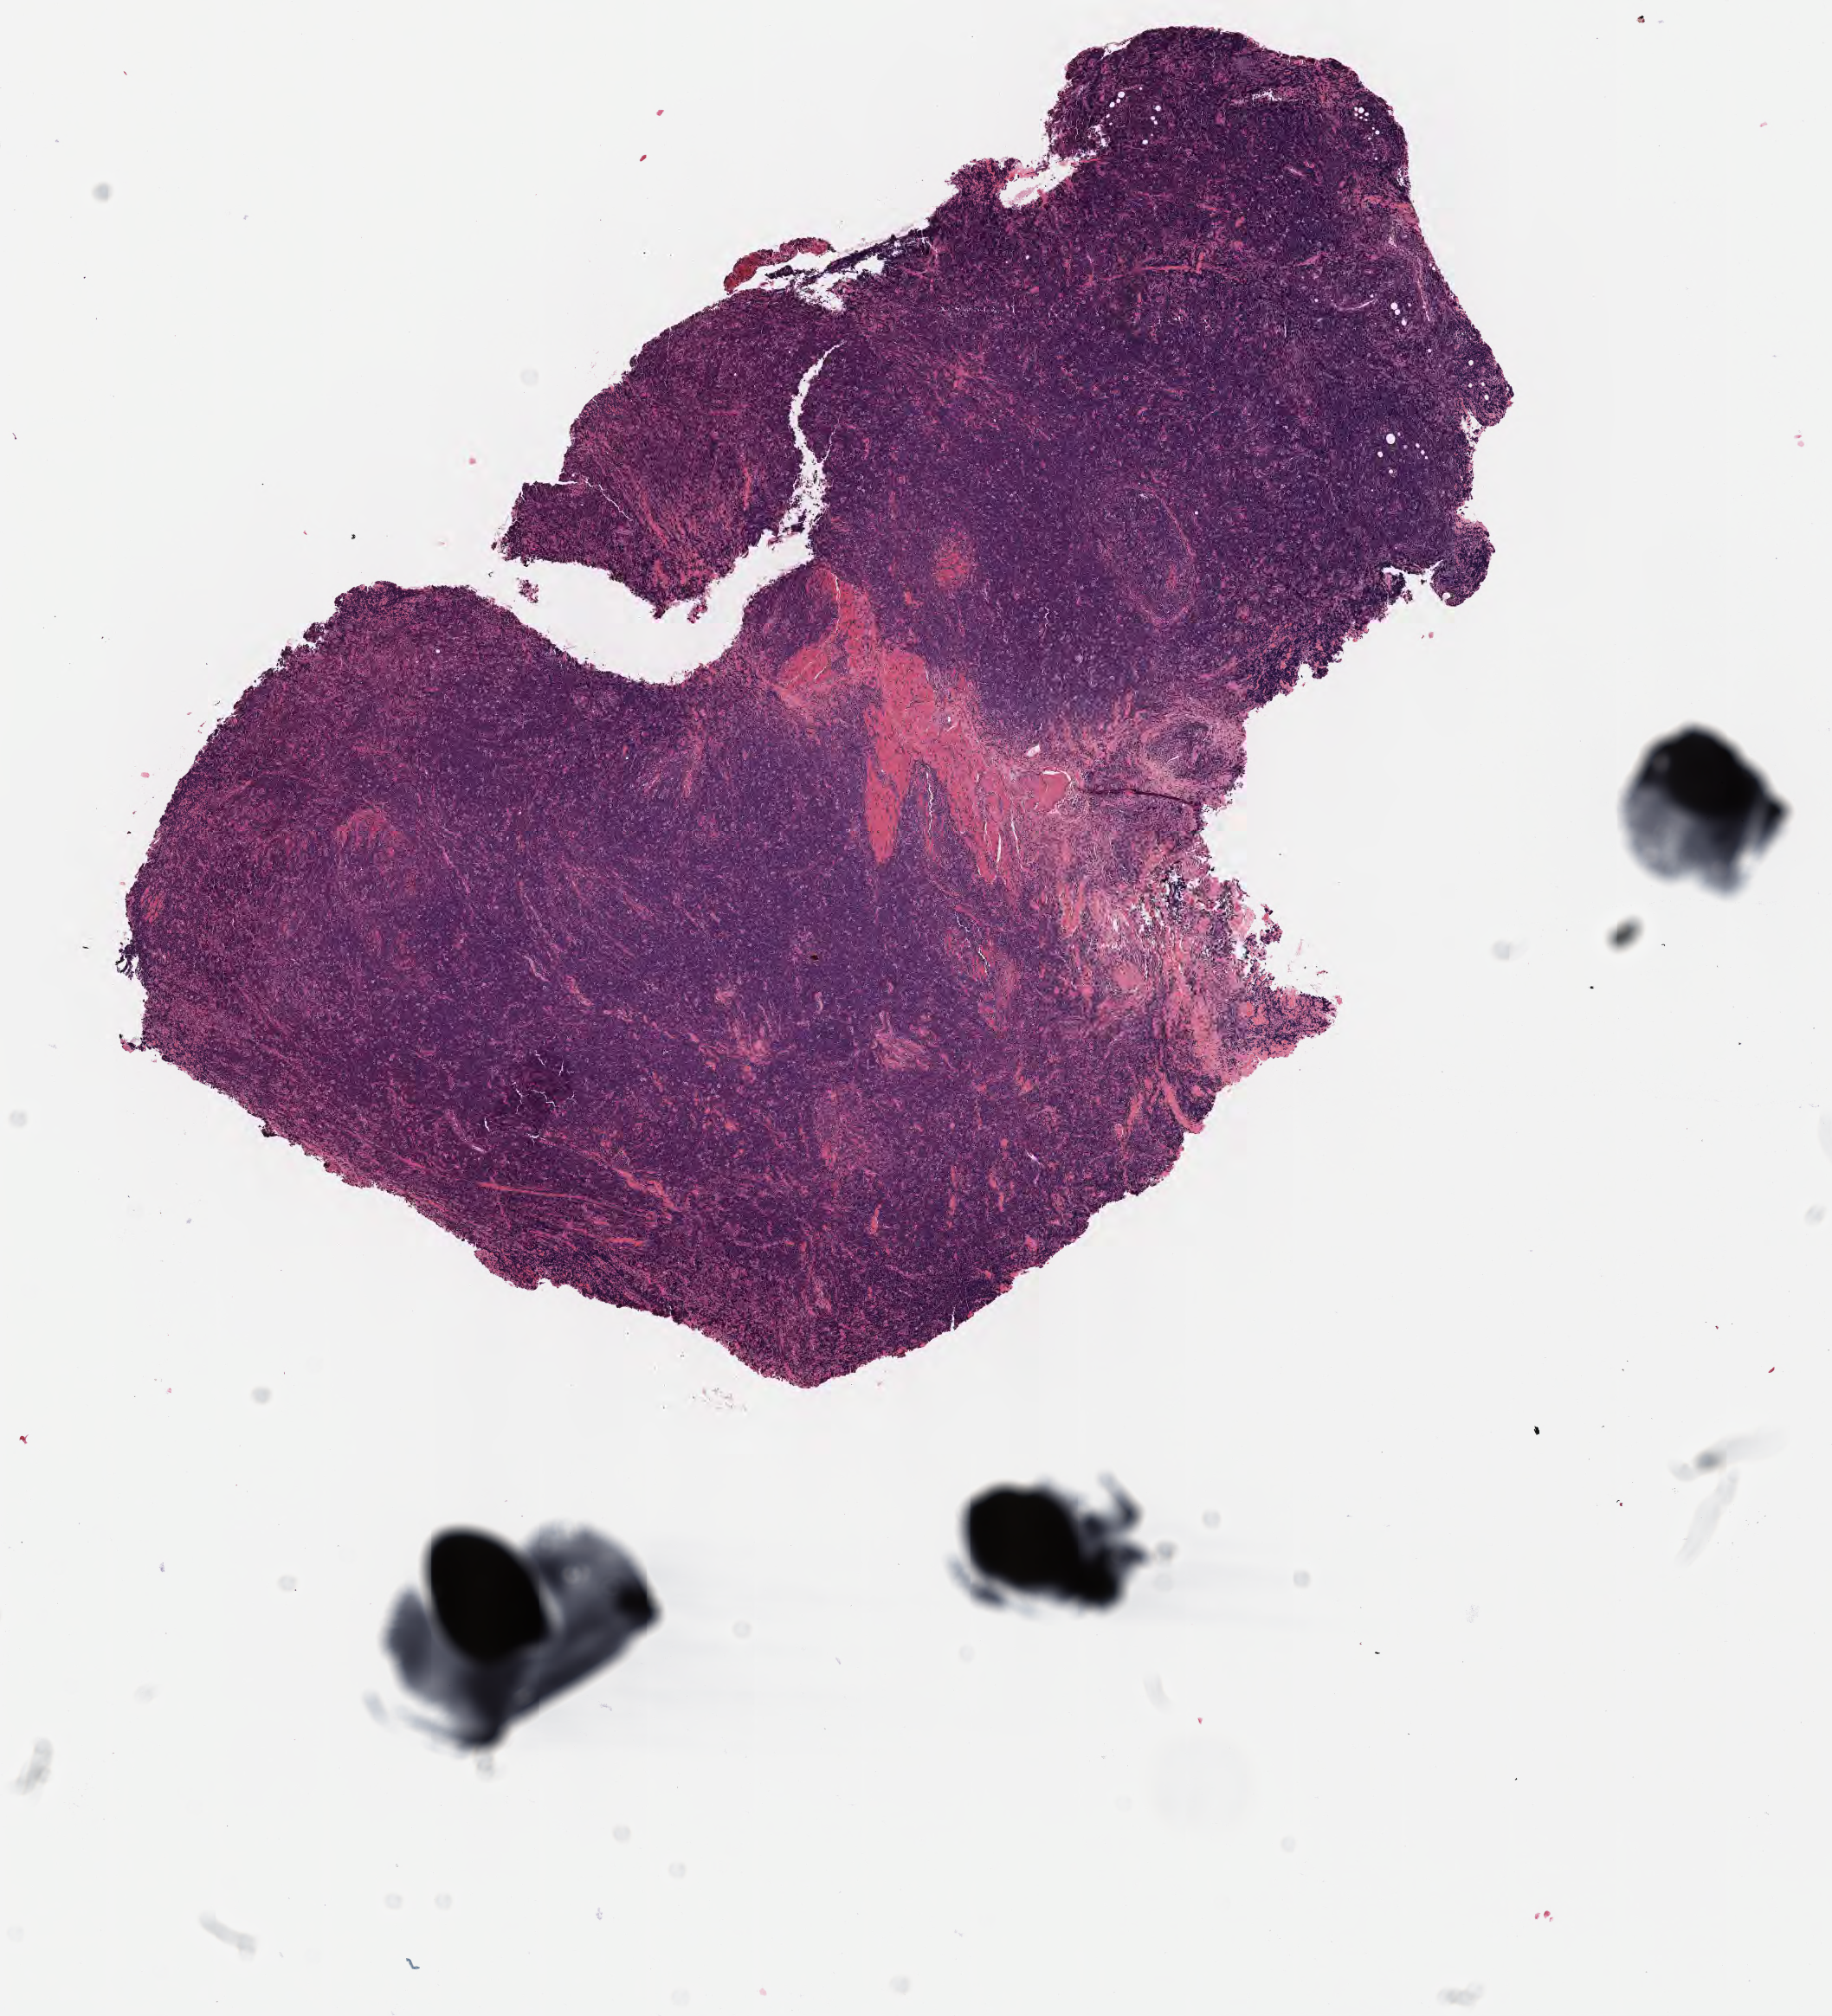
Digitized H&E-stained section — a low-resolution overview of the entire scanned area, about 8.6 x 9.4 mm, tumor tissue, anatomic site: cranium. Male patient; age at initial diagnosis 6 years.
- diagnosis: Diffuse large B-cell lymphoma, NOS